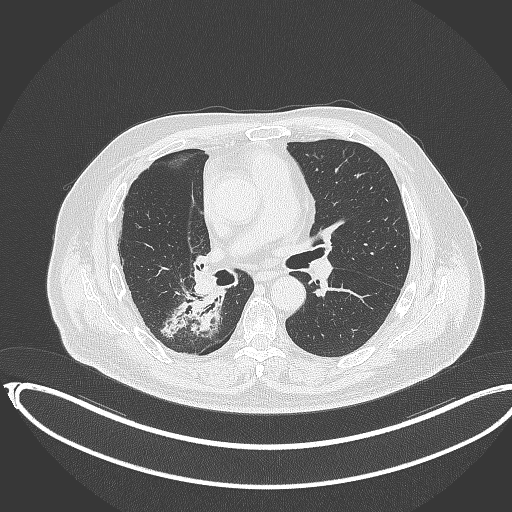
Chest CT, one axial slice. Slice 191 of 403 in the series (ordered by position). Reconstruction kernel B70f. 120 kVp. Lung window (W 1500 / L -600 HU). 1 mm slice thickness. 512 × 512 image matrix, field of view 436 × 436 mm. Patient: male, 68 years. From the clinical record (not read from this slice): clinical TNM (as recorded): T2a N0 M0.
Annotated regions visible in this slice (rectangle marked by the reading radiologist):
- lung tumour (recorded histology: adenocarcinoma): bounding box (x1, y1, x2, y2) in pixels: (161, 287, 228, 336)